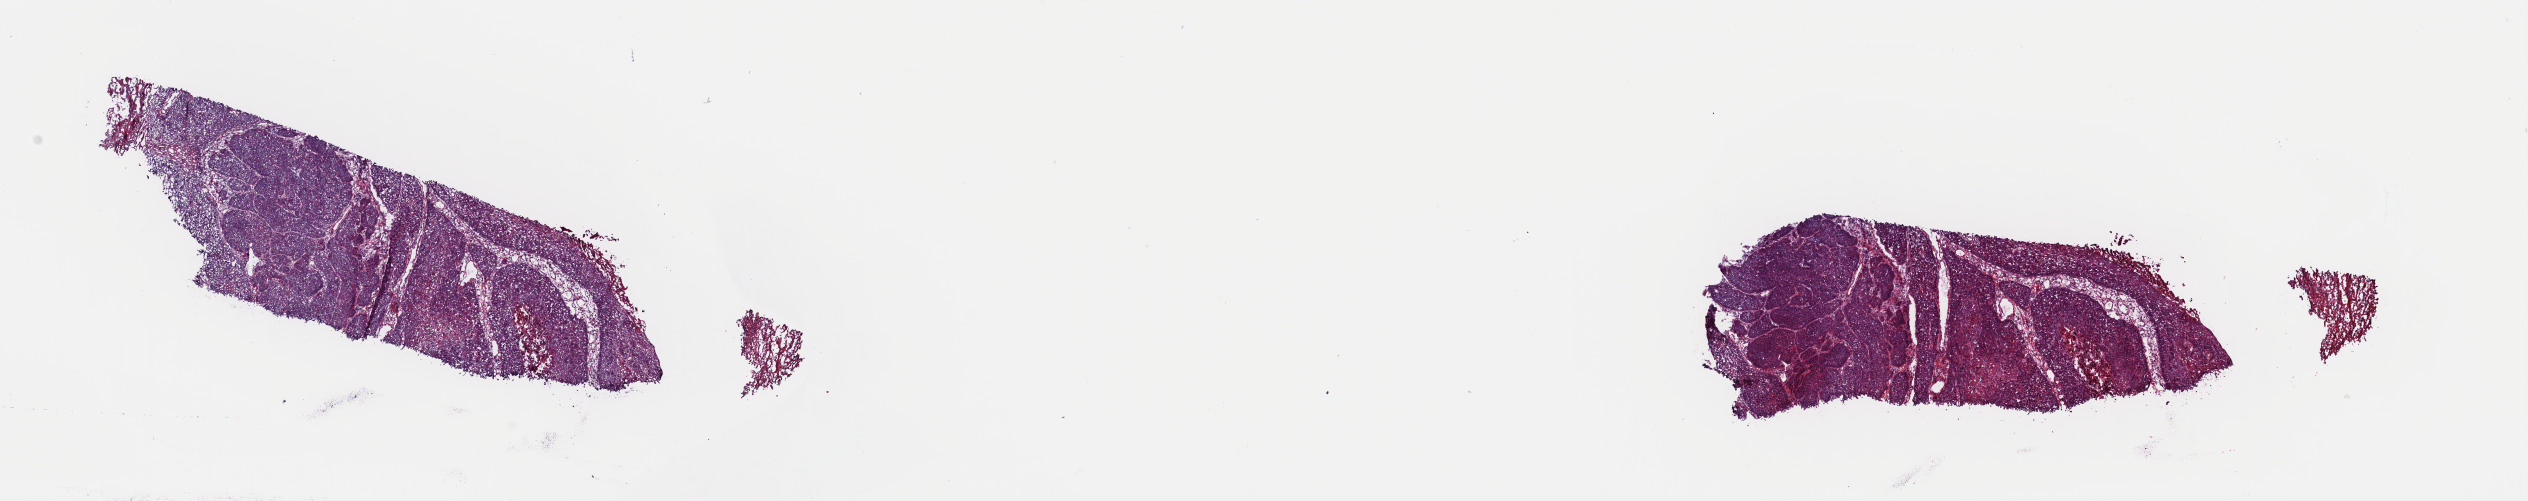
Whole-slide histology image, Hematoxylin and eosin (H&E) stained, shown as a low-resolution overview of the whole scanned area (about 20.0 x 4.0 mm). Frozen section. Esophagus, primary tumour sample. Male patient; age at initial diagnosis 46 years. Histologic grade: G1 (well differentiated). Composition of this section per pathologist review: tumour cells 90%, tumour nuclei 100%, normal cells 0%, stromal cells 8%, necrosis 2%. Inflammatory infiltration, as recorded: lymphocyte infiltration 2%, monocyte infiltration 1%, neutrophil infiltration 0%.
TNM: T2 N0 M0. Histologic diagnosis: Squamous cell carcinoma, NOS. AJCC pathologic stage: IIA (6th edition).